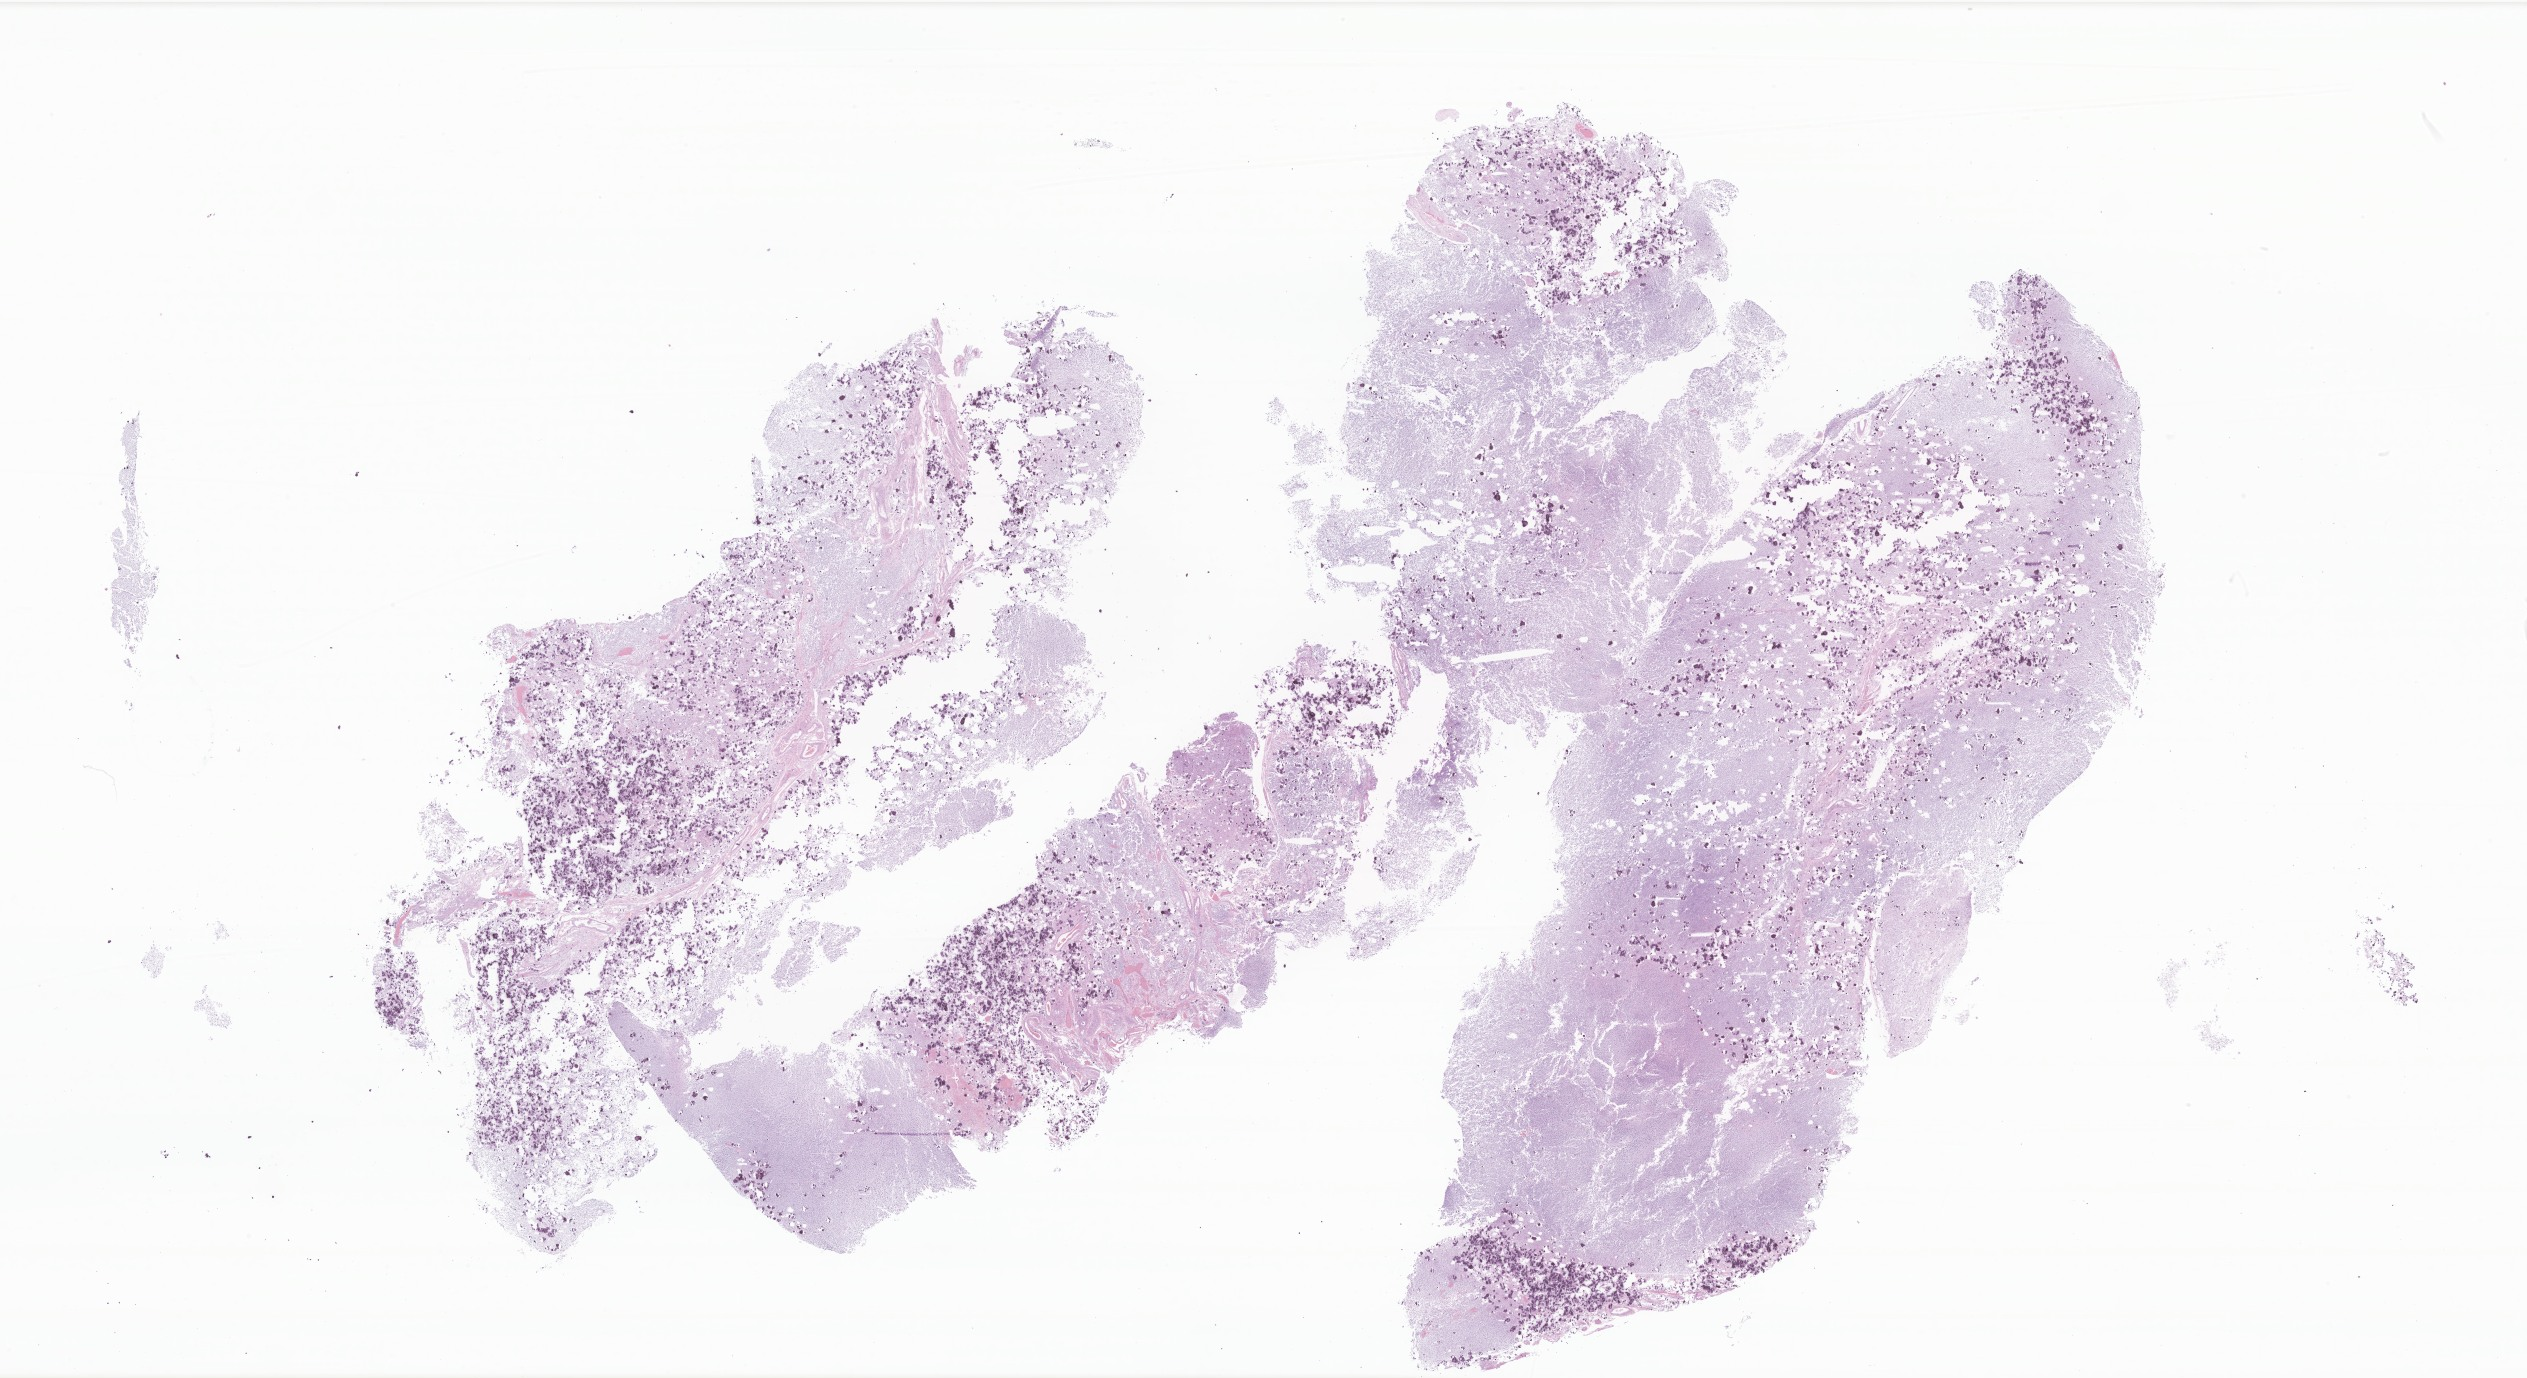
Whole-slide image, haematoxylin and eosin stain of tumor tissue from the brain, whole scanned area (about 42.6 x 23.2 mm) shown as a low-resolution overview, FFPE section. Female patient, age 159 months.
* diagnosis (ICD-O-3 morphology term): Neoplasm, uncertain whether benign or malignant